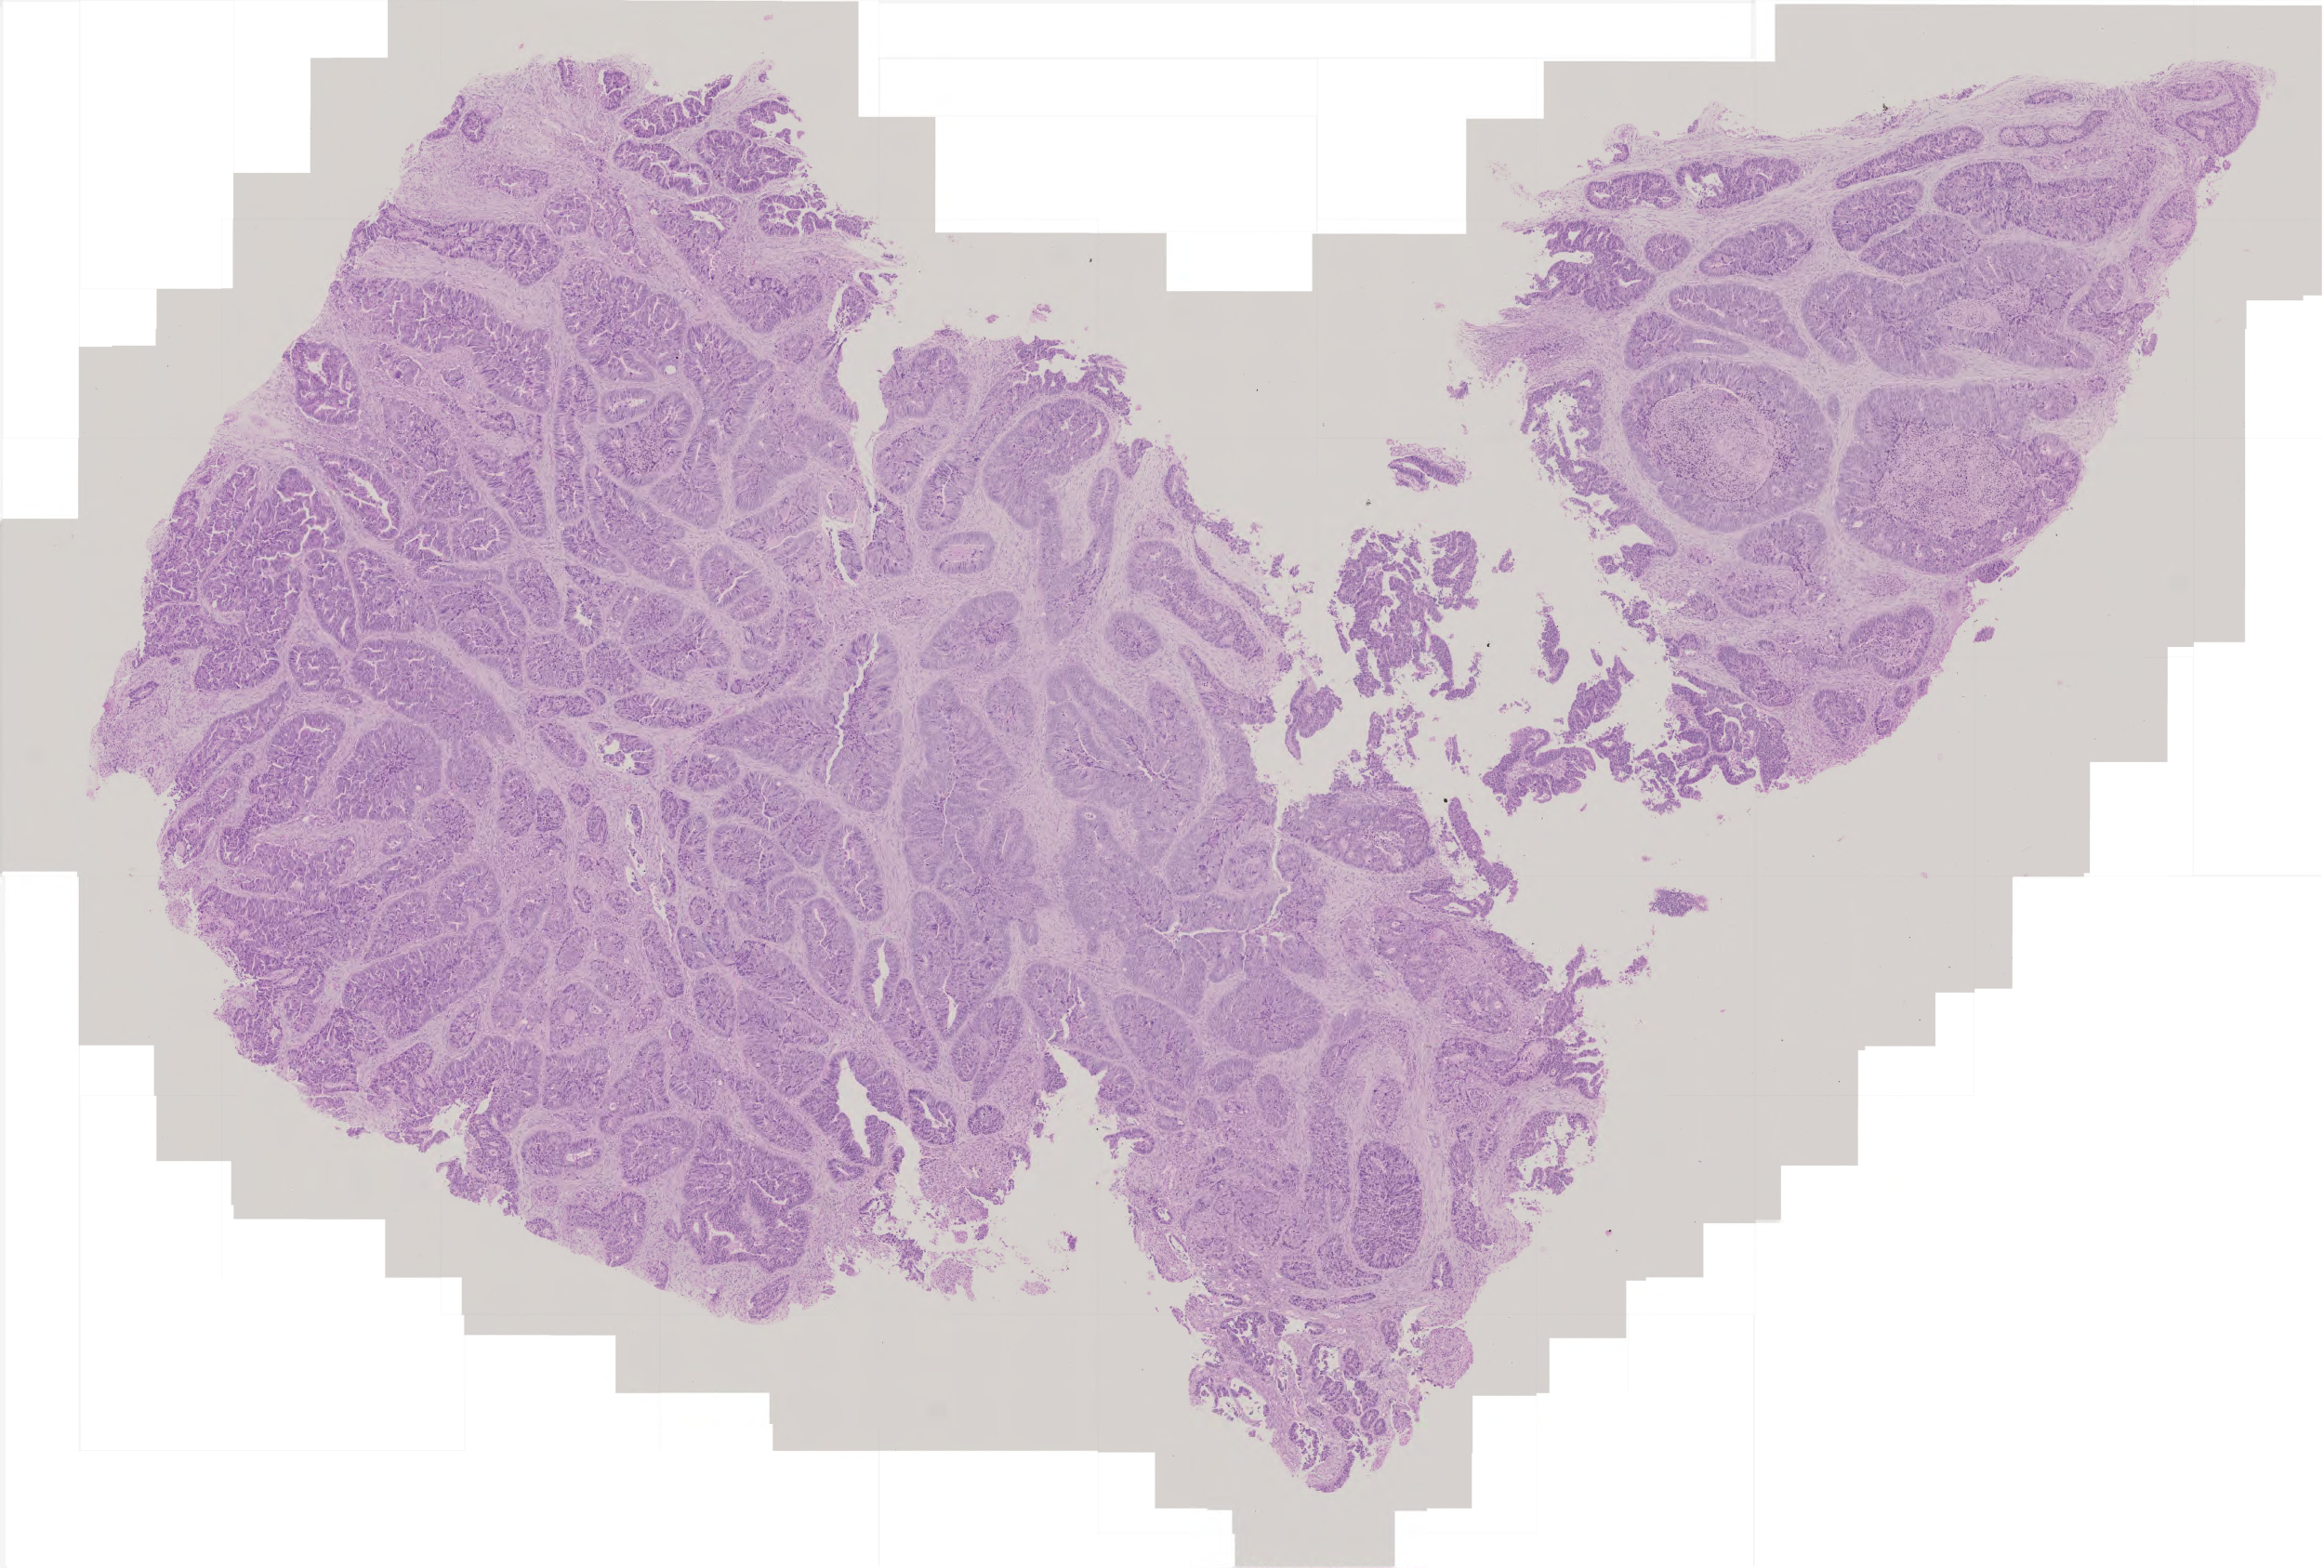
H&E-stained whole-slide image, whole scanned area (about 5.0 x 3.4 mm) shown as a low-resolution overview, formalin-fixed paraffin-embedded (FFPE) diagnostic section, colon, primary tumour sample. Patient: female, age at initial diagnosis 51 years.
AJCC pathologic stage: II. Histologic diagnosis: Adenocarcinoma, NOS.